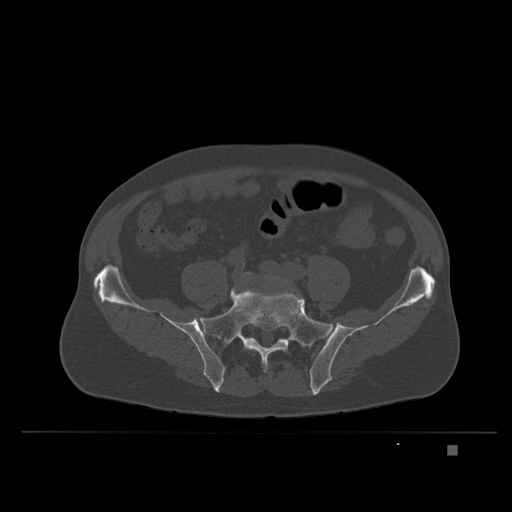
CT including the spine, one axial slice; position 41 of 435 along the scan axis; bone window (W 1800 / L 400 HU); 512 × 512 image matrix, field of view 434 × 434 mm. Male patient, age 73 years. Case-level facts recorded for this patient, not image findings: primary cancer: skin.
Structures marked on this image (semi-automatic segmentation, software-assisted and operator-edited):
- L5 vertebra: box from (x=240, y=272) to (x=289, y=356) px